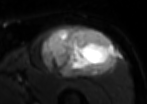
MRI of an extremity soft-tissue mass, one axial slice. Position 59 of 85 along the scan axis. T2-weighted fat-saturated. MR volume resampled by the dataset authors to the PET/CT grid (not the native acquisition matrix). 3.27 mm slice thickness. 147 × 104 image matrix, field of view 144 × 102 mm. Male patient. From the clinical record (not read from this slice): histological type: extraskeletal osteosarcoma; grade: high; site of the primary tumour: thigh.
Structures marked on this image (expert contour drawn on MRI and transferred to this co-registered scan by the dataset authors):
- gross tumour volume (mass): bounding box (x1, y1, x2, y2) in pixels: (40, 26, 118, 77)